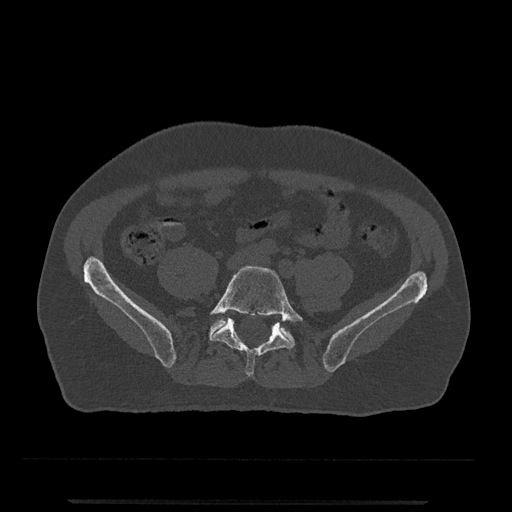
CT including the spine, one axial slice. 120 kVp. Bone window (W 1800 / L 400 HU). 0.5 mm slice thickness. 512 × 512 image matrix, field of view 419 × 419 mm. Male patient, age 63 years. Case-level facts recorded for this patient, not image findings: primary cancer: prostate.
Outlined on this slice (semi-automatic segmentation, software-assisted and operator-edited):
- L5 vertebra: bounding box [x1, y1, x2, y2] px = [209, 266, 306, 377]